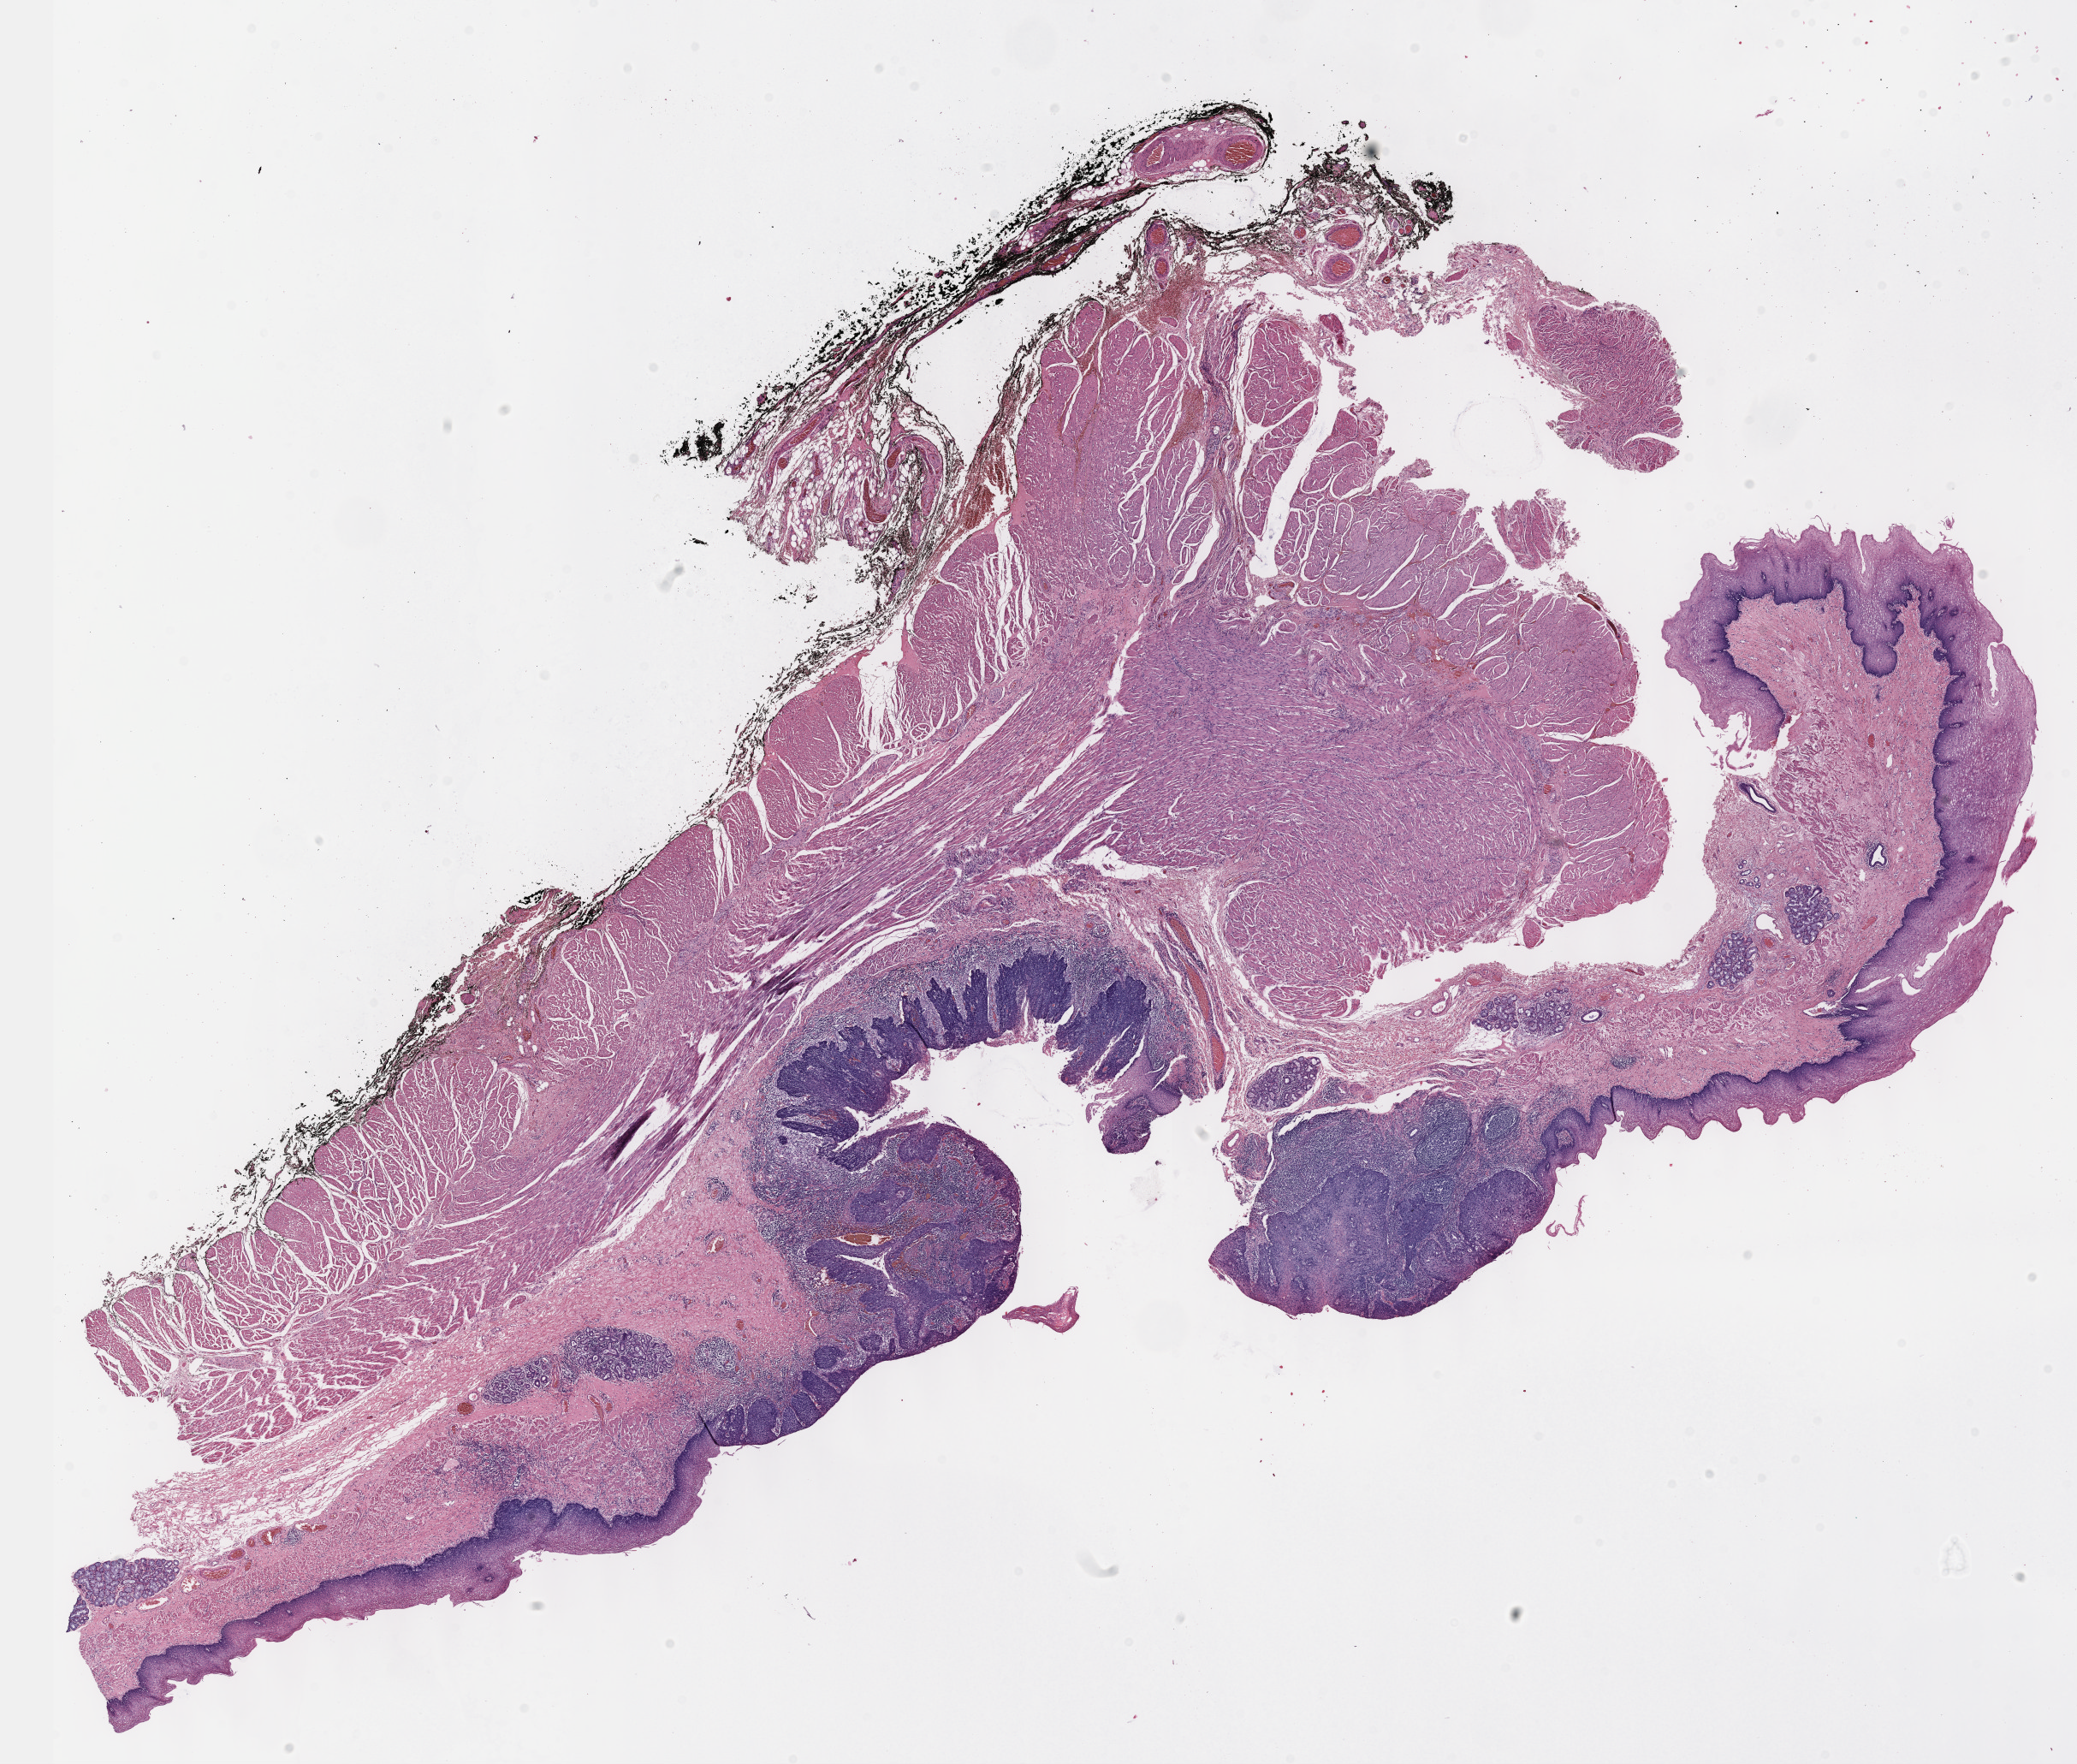
Whole-slide histology image, Hematoxylin and eosin (H&E) stained — low-resolution overview of the scanned area, about 19.6 x 16.7 mm (slide scanned at 40x), FFPE section, sample: primary tumour, esophagus. Male patient; age at initial diagnosis 63 years. Histologic grade: G2 (moderately differentiated).
TNM: T1 N1 M1a. Diagnosis: Squamous cell carcinoma, NOS. AJCC pathologic stage: IVA (6th edition). Lymph nodes positive (case pathology): 9 of 34 examined.